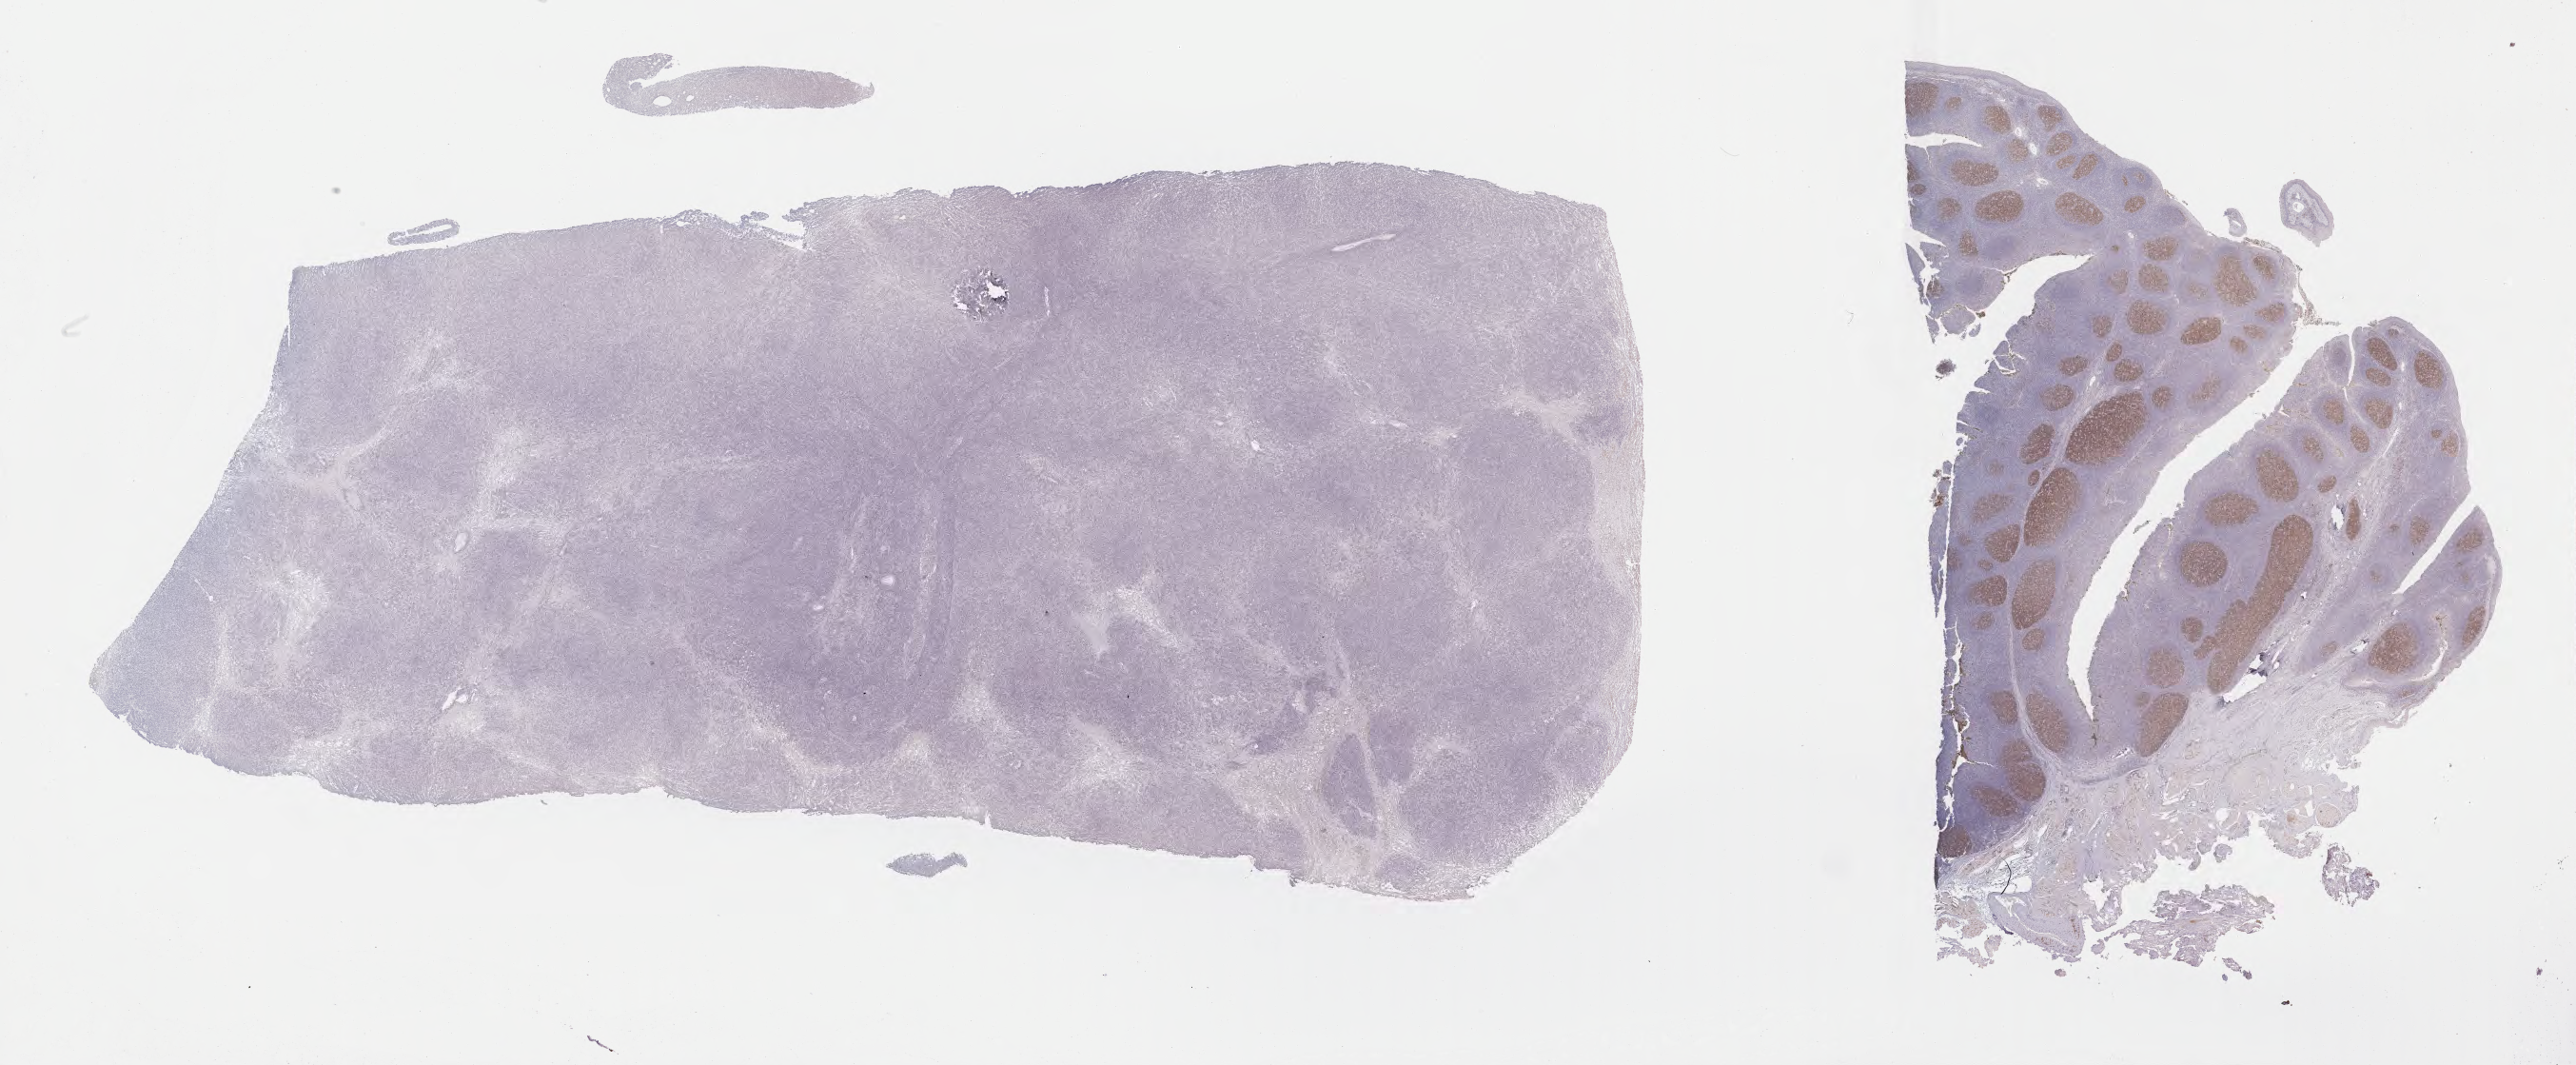
Whole-slide image, immunohistochemical stain for CD10 — shown as a low-resolution overview of the whole scanned area (about 43.8 x 18.1 mm), tumor tissue. Patient male; age 39 years.
Histologic diagnosis: Diffuse large B-cell lymphoma, NOS.